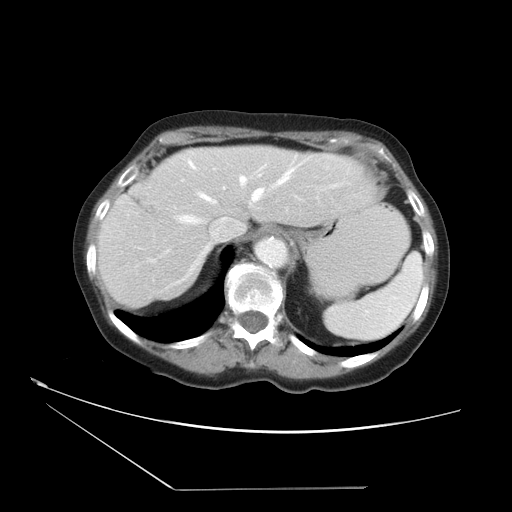
Contrast-enhanced abdominal CT, one axial slice; position 27 of 36 along the scan axis; soft-tissue window (W 400 / L 40 HU); 5 mm slice thickness; 512 × 512 image matrix, field of view 384 × 384 mm. Female patient, age 81 years. Case-level facts recorded for this patient, not image findings: diagnosis: colorectal cancer liver metastases, imaged before liver resection; multiple liver metastases: no; largest metastasis: 1.6 cm; disease in both lobes: no.
Structures marked on this image (outlined manually by an expert reader):
- hepatic veins: bounding box <175,158,309,284> (left, top, right, bottom; pixels)
- liver: <98,146,379,308>
- planned liver remnant (the part of the liver to remain after resection): <98,146,379,309>